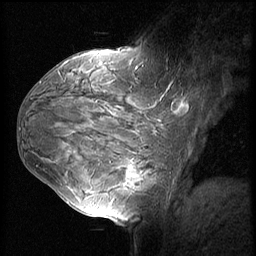
Breast MRI (dynamic contrast-enhanced), one sagittal slice. Slice 34 of 60 in the series (ordered by position). Dynamic contrast-enhanced series, image 2 of 3 at this slice position (ordered by acquisition). 1.5 T. TE 4.2 ms, TR 8.9 ms. 2.5 mm slice thickness. 256 × 256 image matrix, field of view 220 × 220 mm. Female patient, age 37 years. Case-level facts recorded for this patient, not image findings: setting: breast cancer imaged before/during neoadjuvant chemotherapy; receptor status: triple-negative.
Structures marked on this image (semi-automatically segmented with operator editing):
- analysis volume of interest (the breast-tissue region the enhancement analysis was run in; not a lesion): box from (x=114, y=153) to (x=159, y=206) px
- tumour enhancement mask (voxels above the 140 % enhancement threshold inside the analysis volume of interest): (x=128, y=166)–(x=143, y=183)